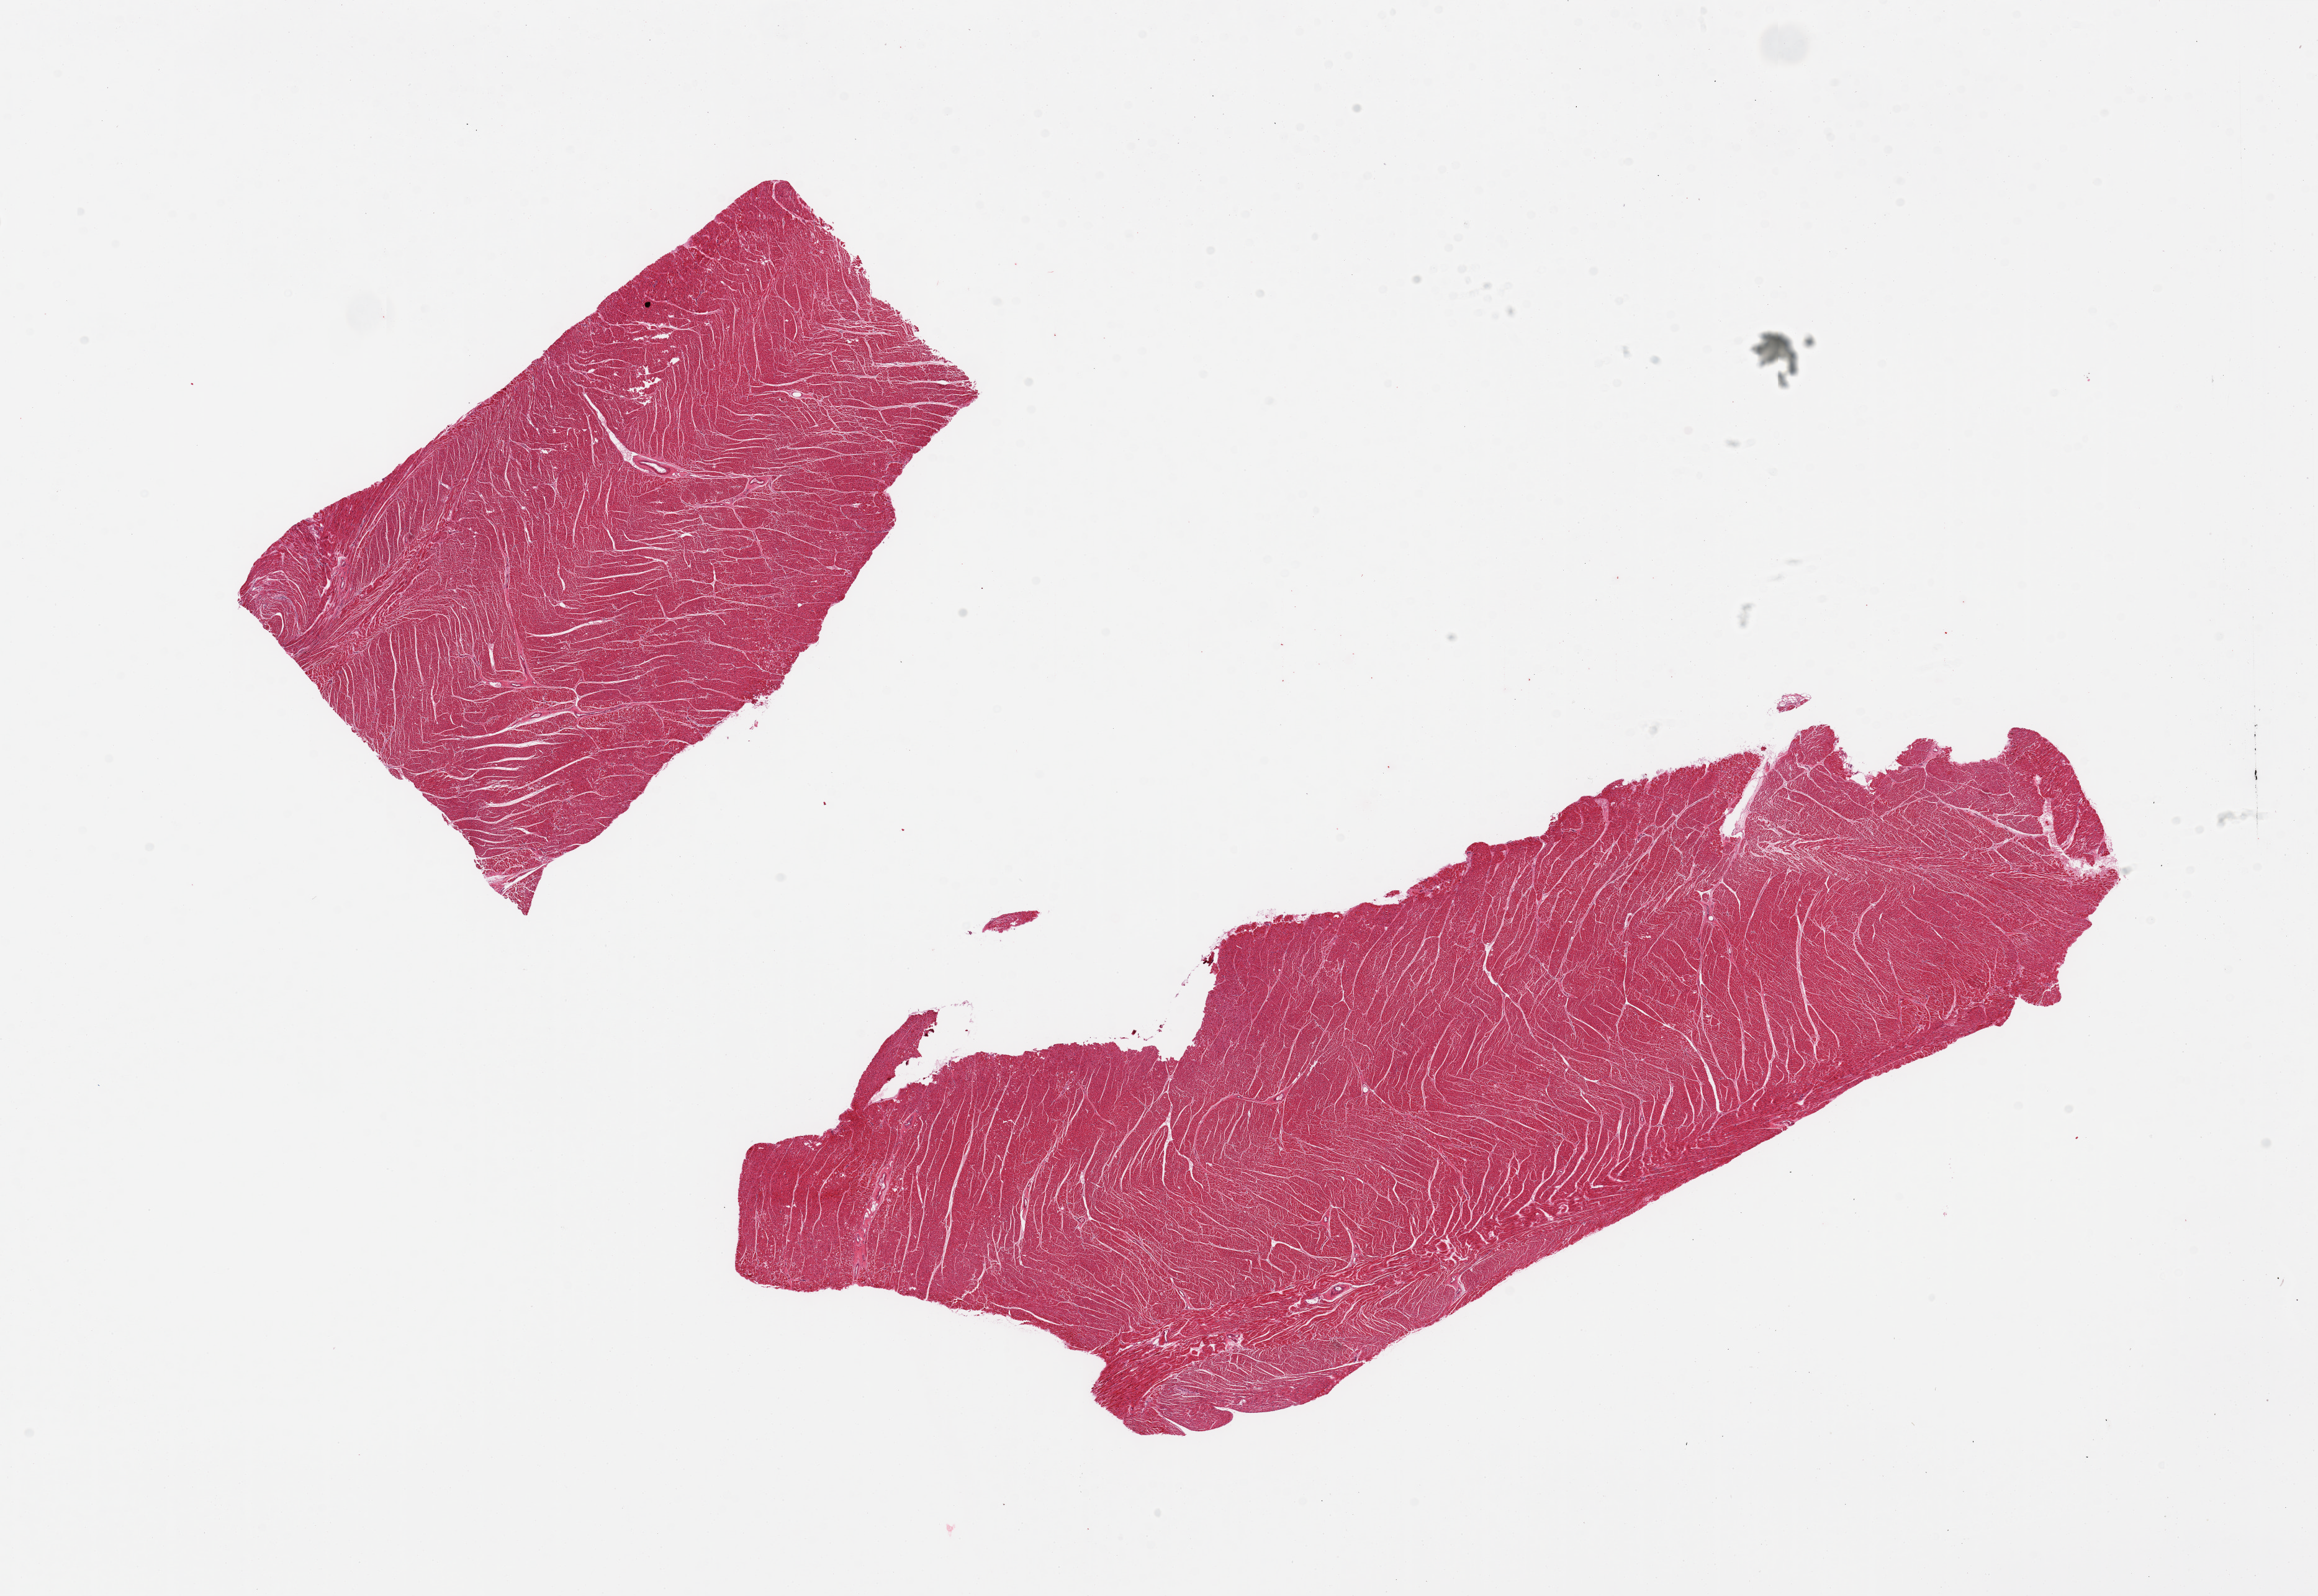
Whole-slide image, hematoxylin and eosin (H&E) stain, shown as a low-resolution overview of the whole scanned area (about 29.5 x 20.3 mm). PAXgene-fixed paraffin-embedded (PFPE) section. Sampled site (target tissue): heart. Donor tissue sample. Donor: female.
* reviewer comment on this tissue sample: 2 pieces, one piece is over-sized up to 18mm